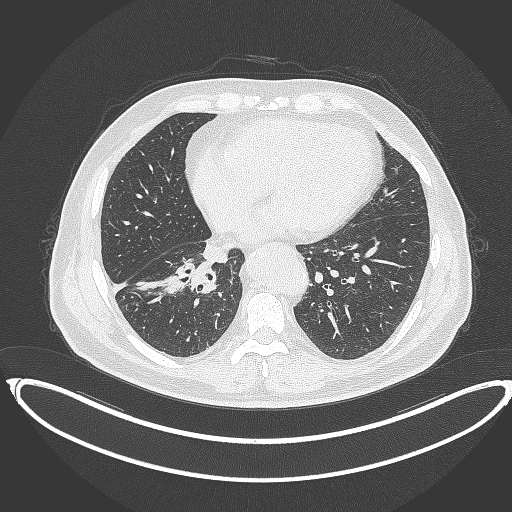
Chest CT, one axial slice; position 153 of 387 along the scan axis; reconstruction kernel B70f; 120 kVp; lung window (W 1500 / L -600 HU); 1 mm slice thickness; 512 × 512 image matrix, field of view 448 × 448 mm. Patient: male, 61 years. Case-level facts recorded for this patient, not image findings: clinical TNM (as recorded): T1b N1 M0.
Structures marked on this image (bounding box drawn by a radiologist):
- lung tumour (recorded histology: squamous cell carcinoma): bounding box (x1, y1, x2, y2) in pixels: (163, 259, 219, 298)